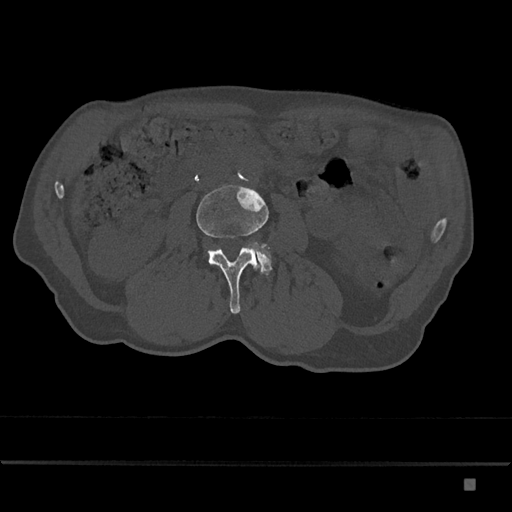
CT including the spine, one axial slice; slice 395 of 797 in the series (ordered by position); bone window (W 1800 / L 400 HU); 0.5 mm slice thickness; 512 × 512 image matrix, field of view 390 × 390 mm. Male patient, age 72 years. Case-level facts recorded for this patient, not image findings: primary cancer: prostate.
Annotated regions visible in this slice (semi-automatically segmented with operator editing):
- L3 vertebra: bounding box <196,185,269,314> (left, top, right, bottom; pixels)
- L4 vertebra: <242,244,272,275>